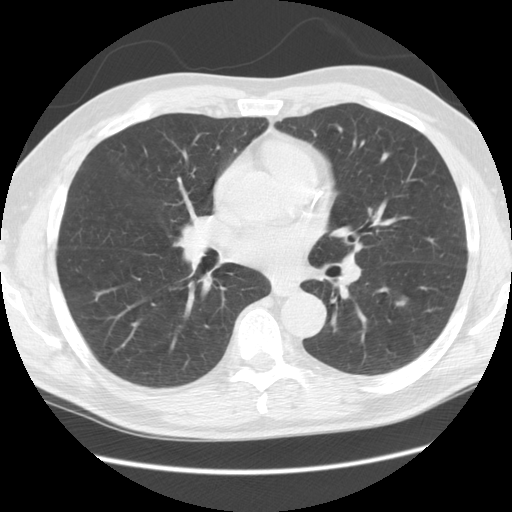
Axial slice from a low-dose chest CT screening exam. Third screening round (two years after baseline). Lung window (W 1500 / L -600 HU). 2.5 mm slice thickness. Standard (soft-tissue) reconstruction kernel (STANDARD). Male participant, aged 60 years at enrolment. Current smoker at enrolment.
- Expert-annotated lung lesion, bounding box <382,289,417,320> (left, top, right, bottom; pixels).
- The screening reader recorded 5 non-calcified nodules or masses ≥4 mm on this exam (left lower lobe, right lower lobe, right lower lobe, left lower lobe, left upper lobe); which of them this box marks is not recorded.
- Participant outcome: lung cancer diagnosed 153 days after this screen — large cell neuroendocrine carcinoma, left lower lobe, poorly differentiated (G3), stage IB (AJCC 6th edition), 33 mm at pathology.